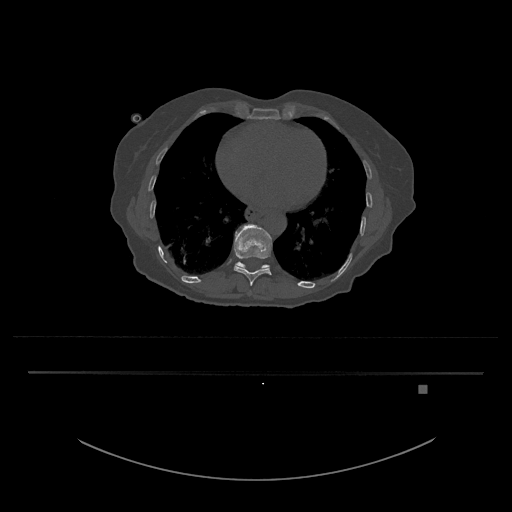
CT including the spine, one axial slice; slice 703 of 797 in the series (ordered by position); reconstruction kernel Br40s/3; bone window (W 1800 / L 400 HU); 512 × 512 image matrix. Female patient, age 57 years. From the clinical record (not read from this slice): primary cancer: cervical.
Outlined on this slice (semi-automatically segmented with operator editing):
- T10 vertebra: bounding box <233,224,272,286> (left, top, right, bottom; pixels)
- T11 vertebra: <235,262,270,270>